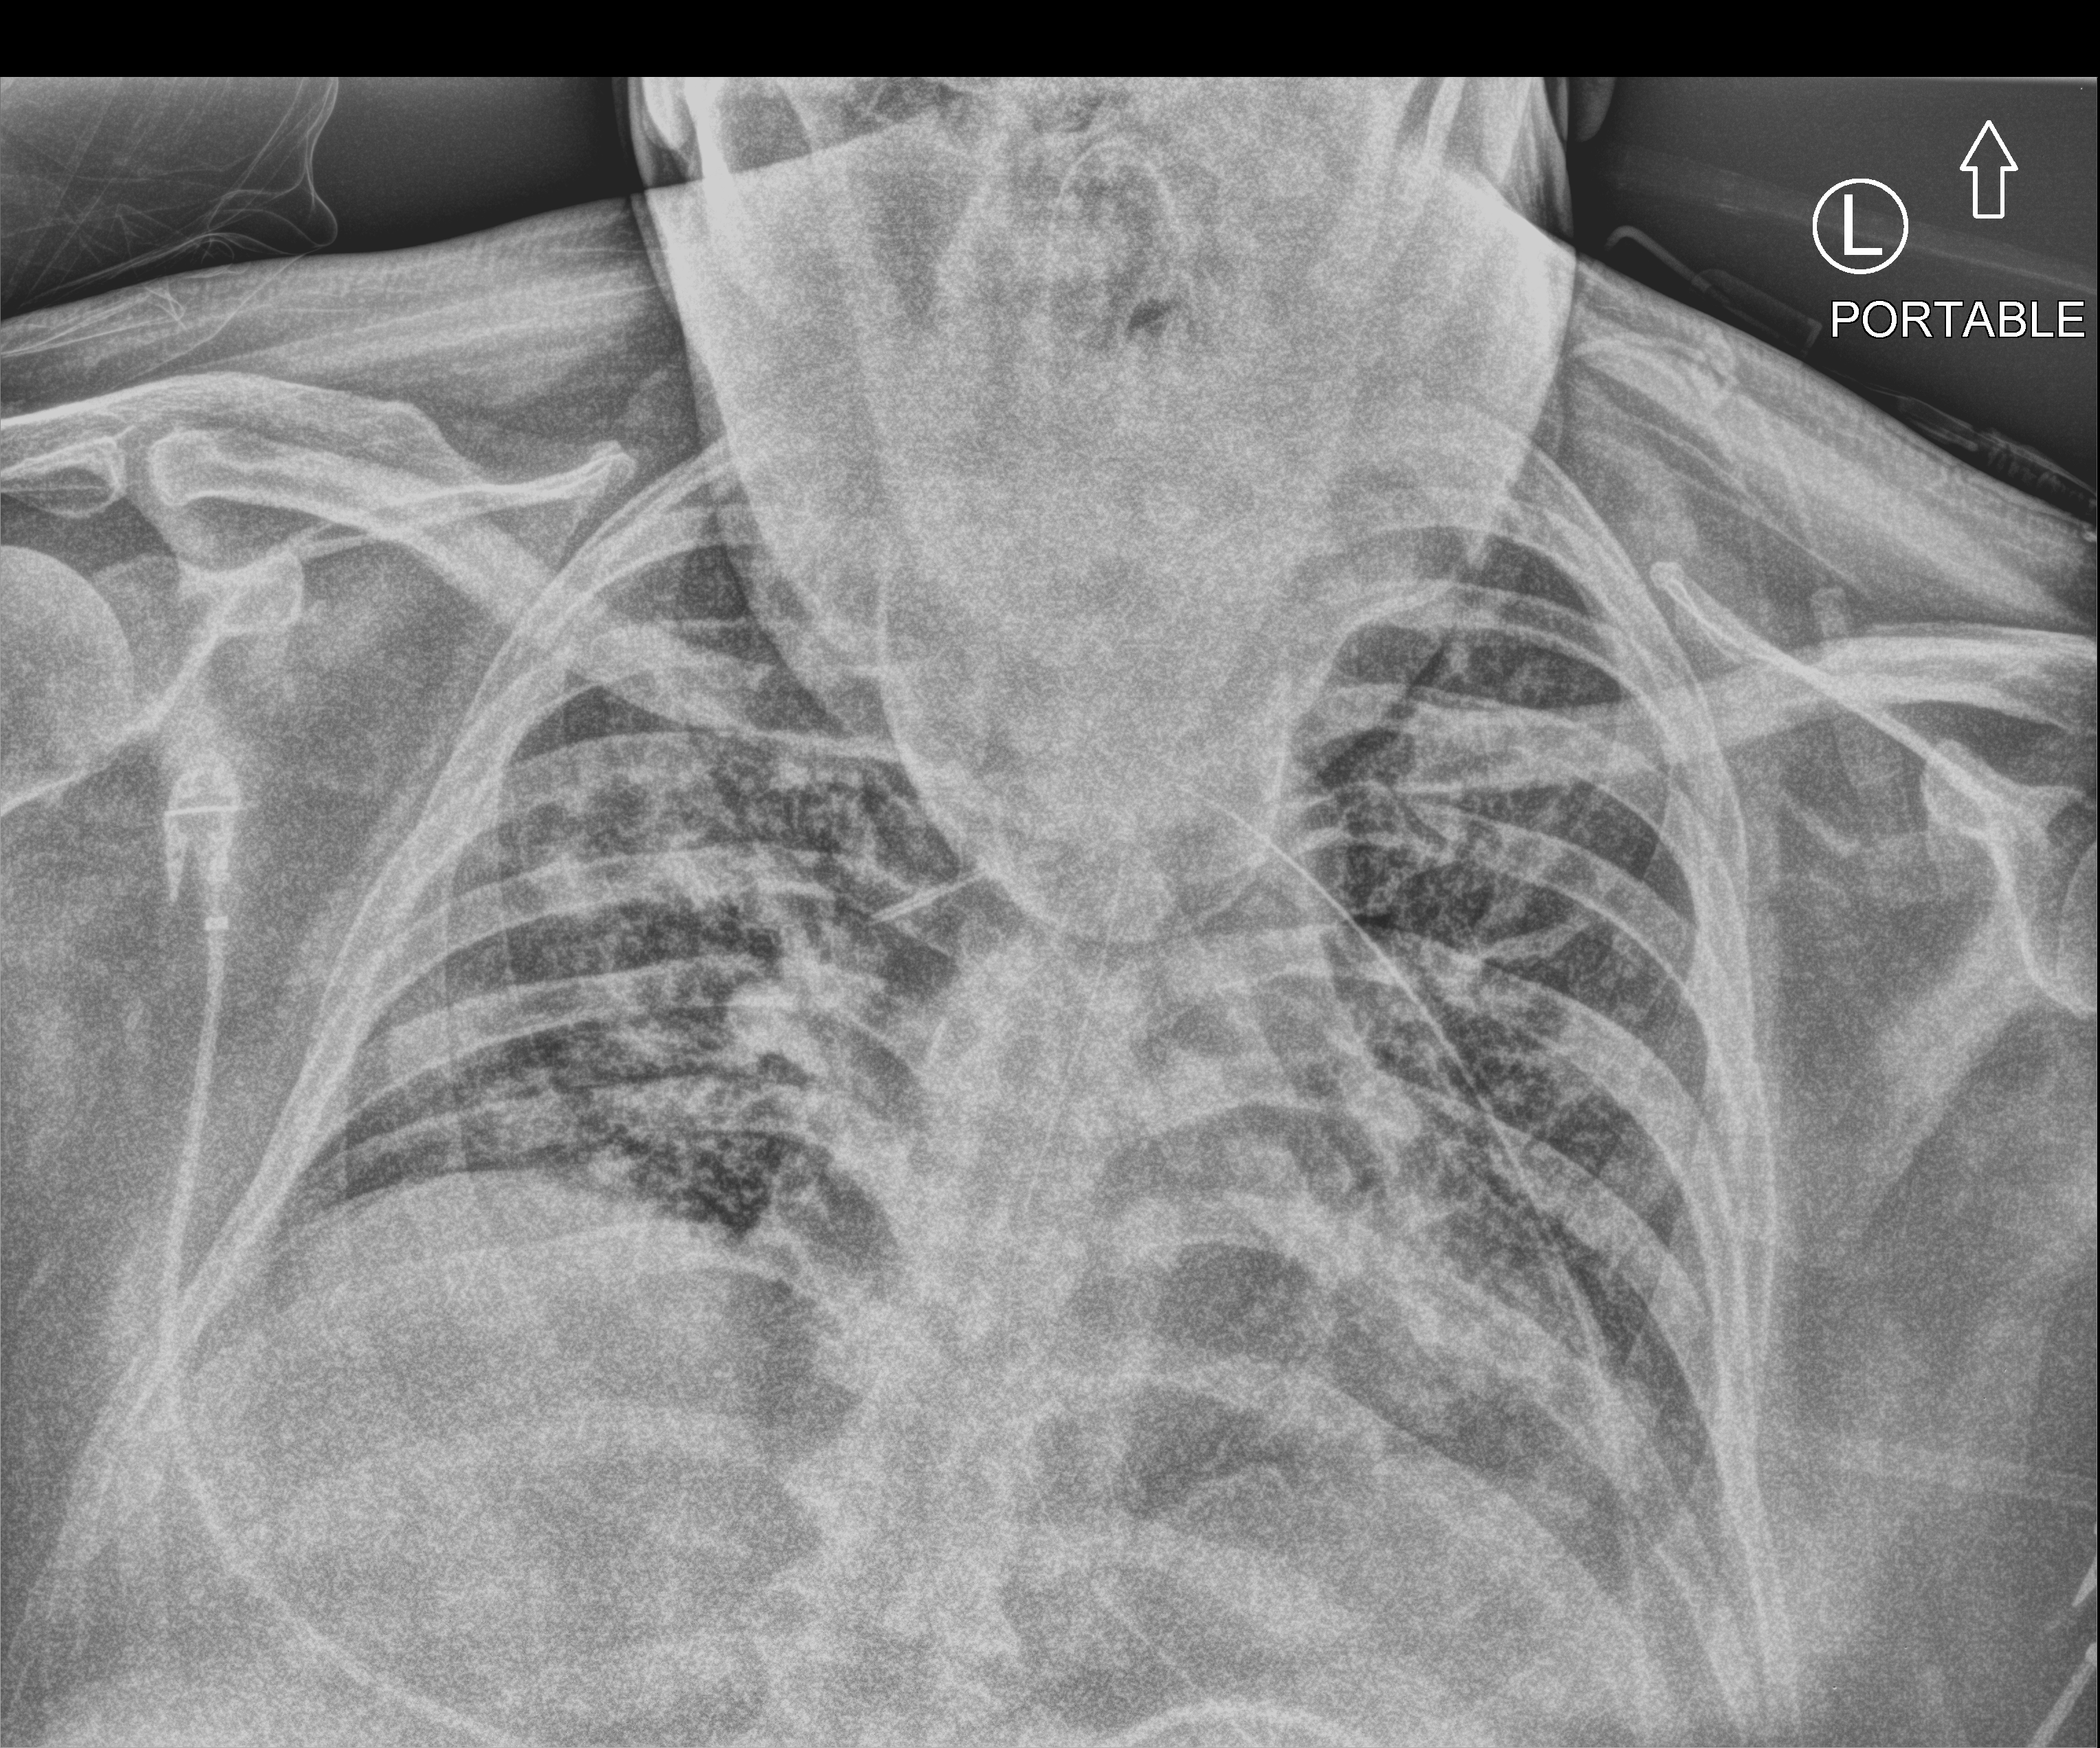
Portable chest radiograph, anteroposterior (AP) projection. Patient hospitalised with COVID-19; male, aged 18–59 years.
Hospital-stay facts (about this admission, not read from this image; timing relative to this image not recorded): admitted to intensive care during this hospital stay: yes.